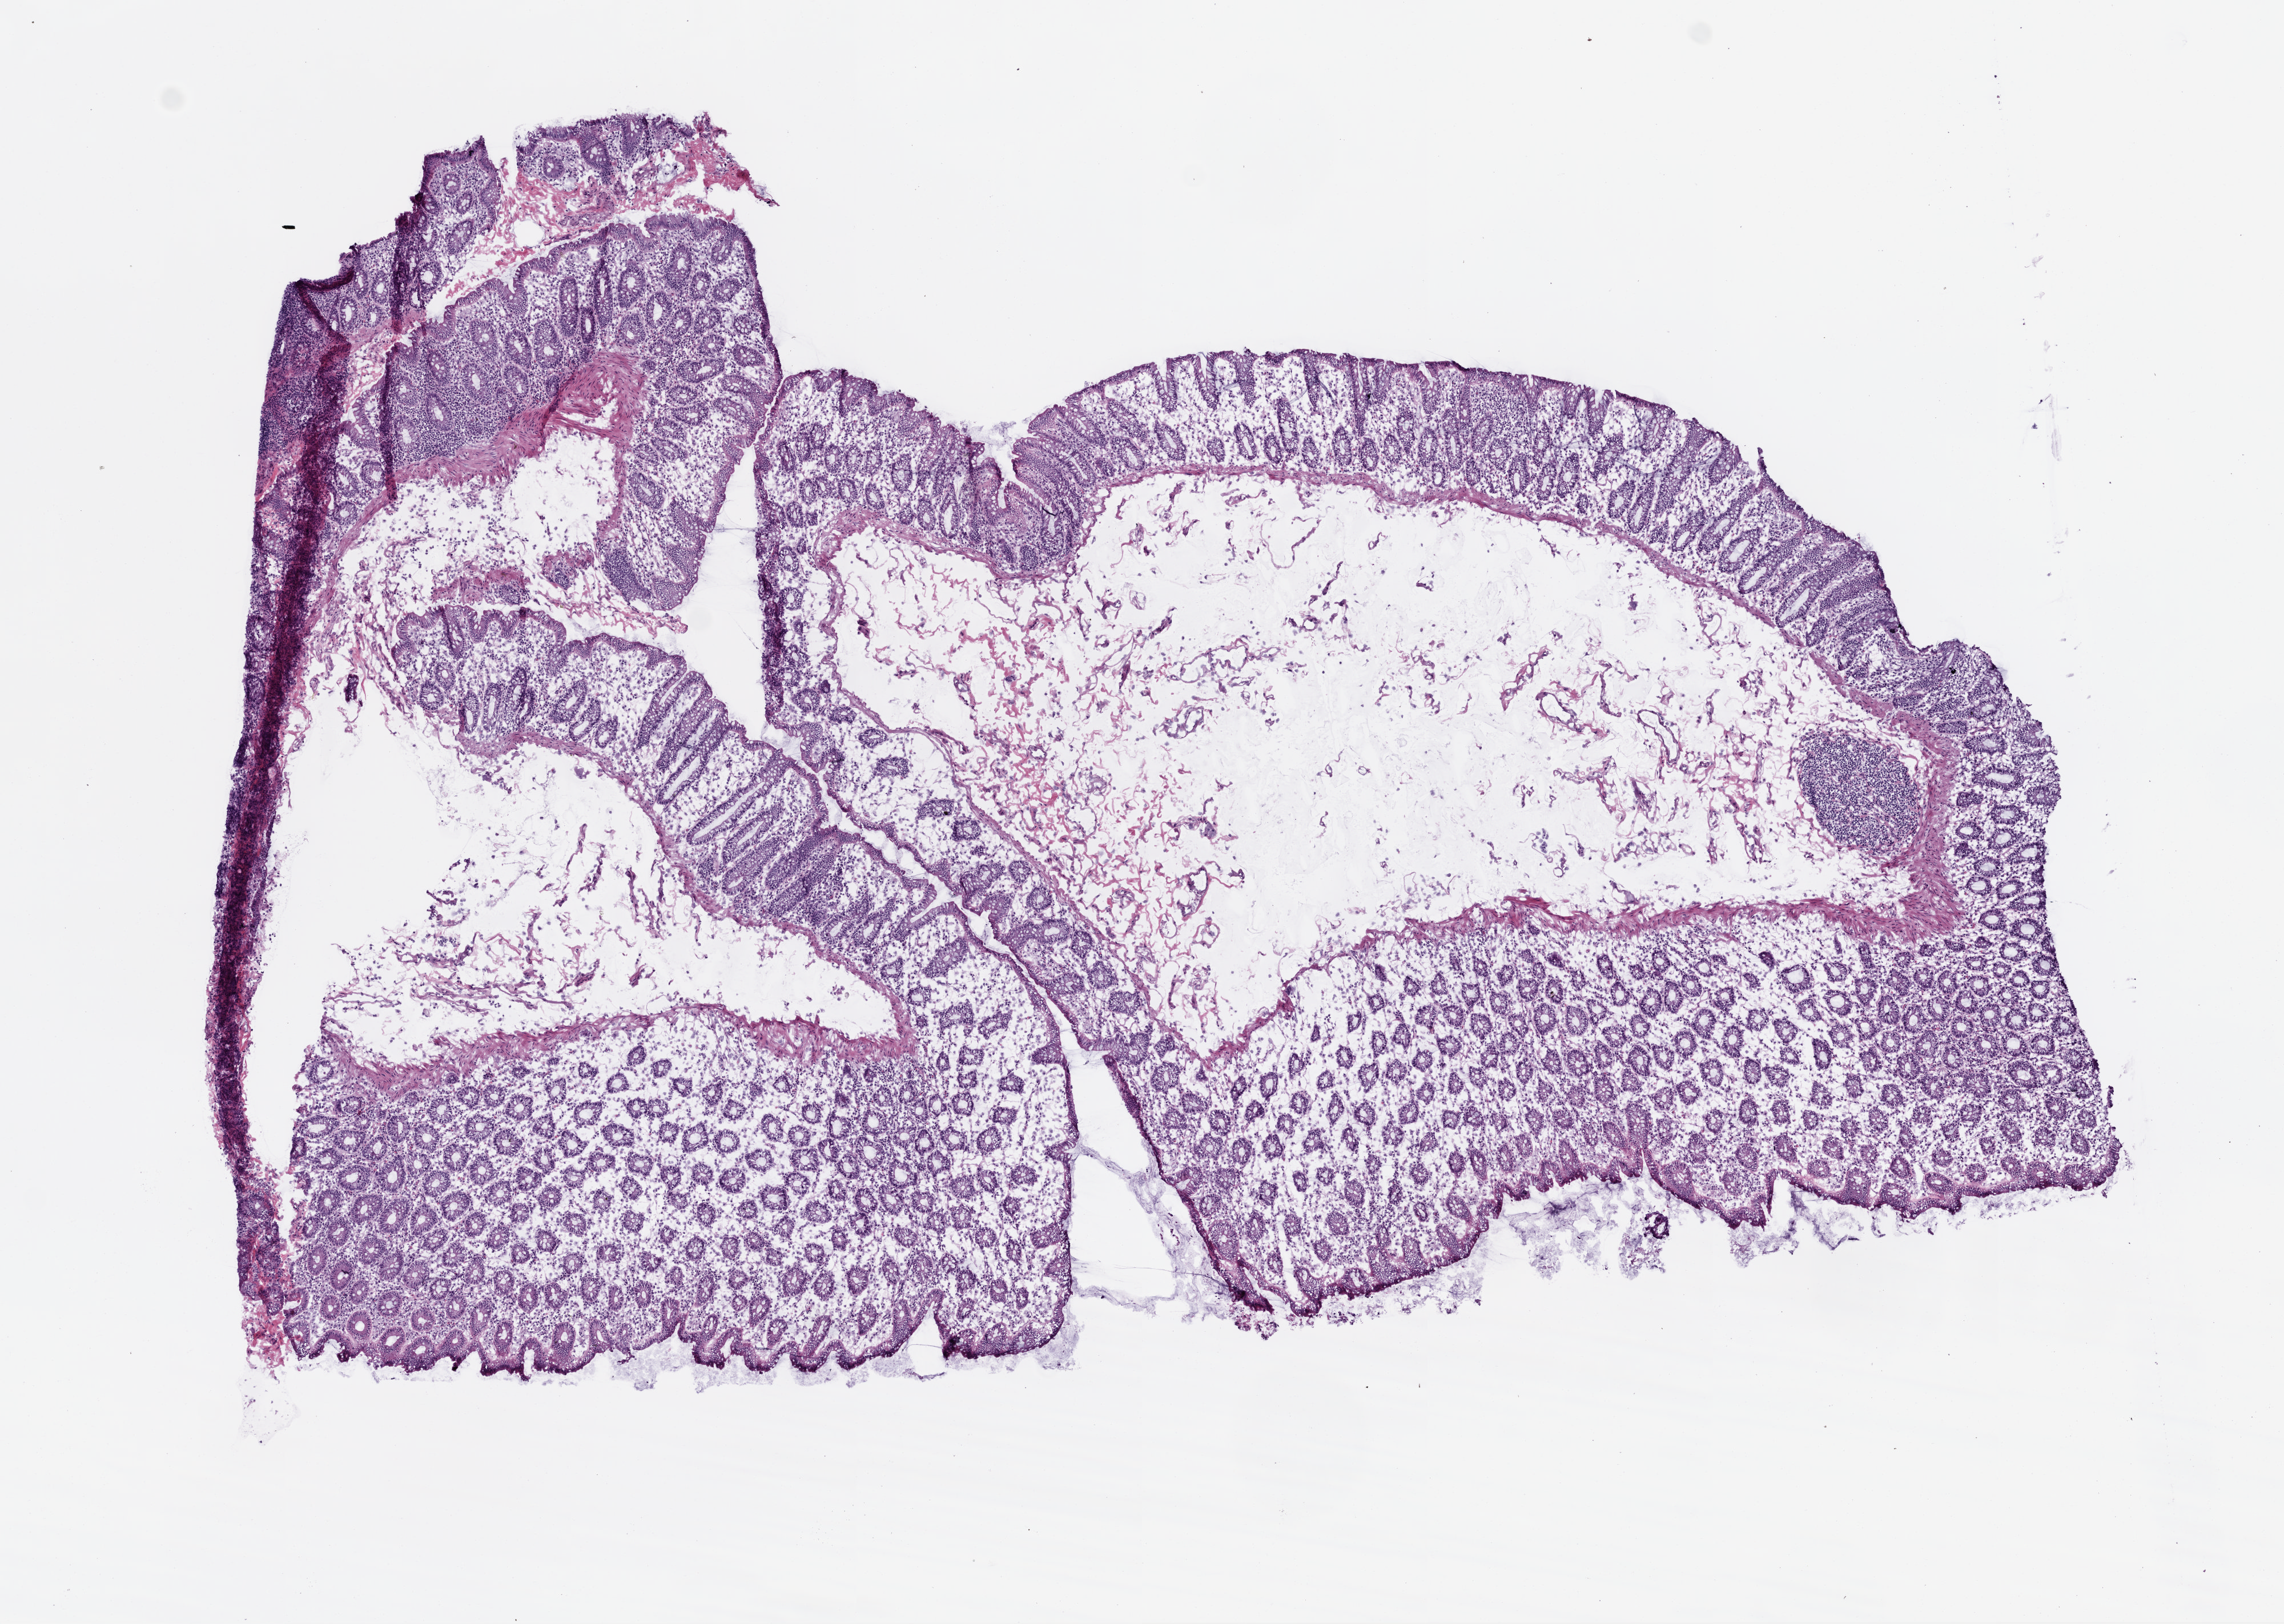
Whole-slide histology image, Hematoxylin and eosin (H&E) stained, shown as a low-resolution overview of the whole scanned area (about 8.0 x 5.7 mm); frozen section from the top of the tissue portion; colon, solid tissue normal (non-tumour tissue) sample. Patient: female, age at initial diagnosis 81 years.
This section: solid tissue normal sample (biorepository sample class). Patient diagnosis: Adenocarcinoma, NOS.